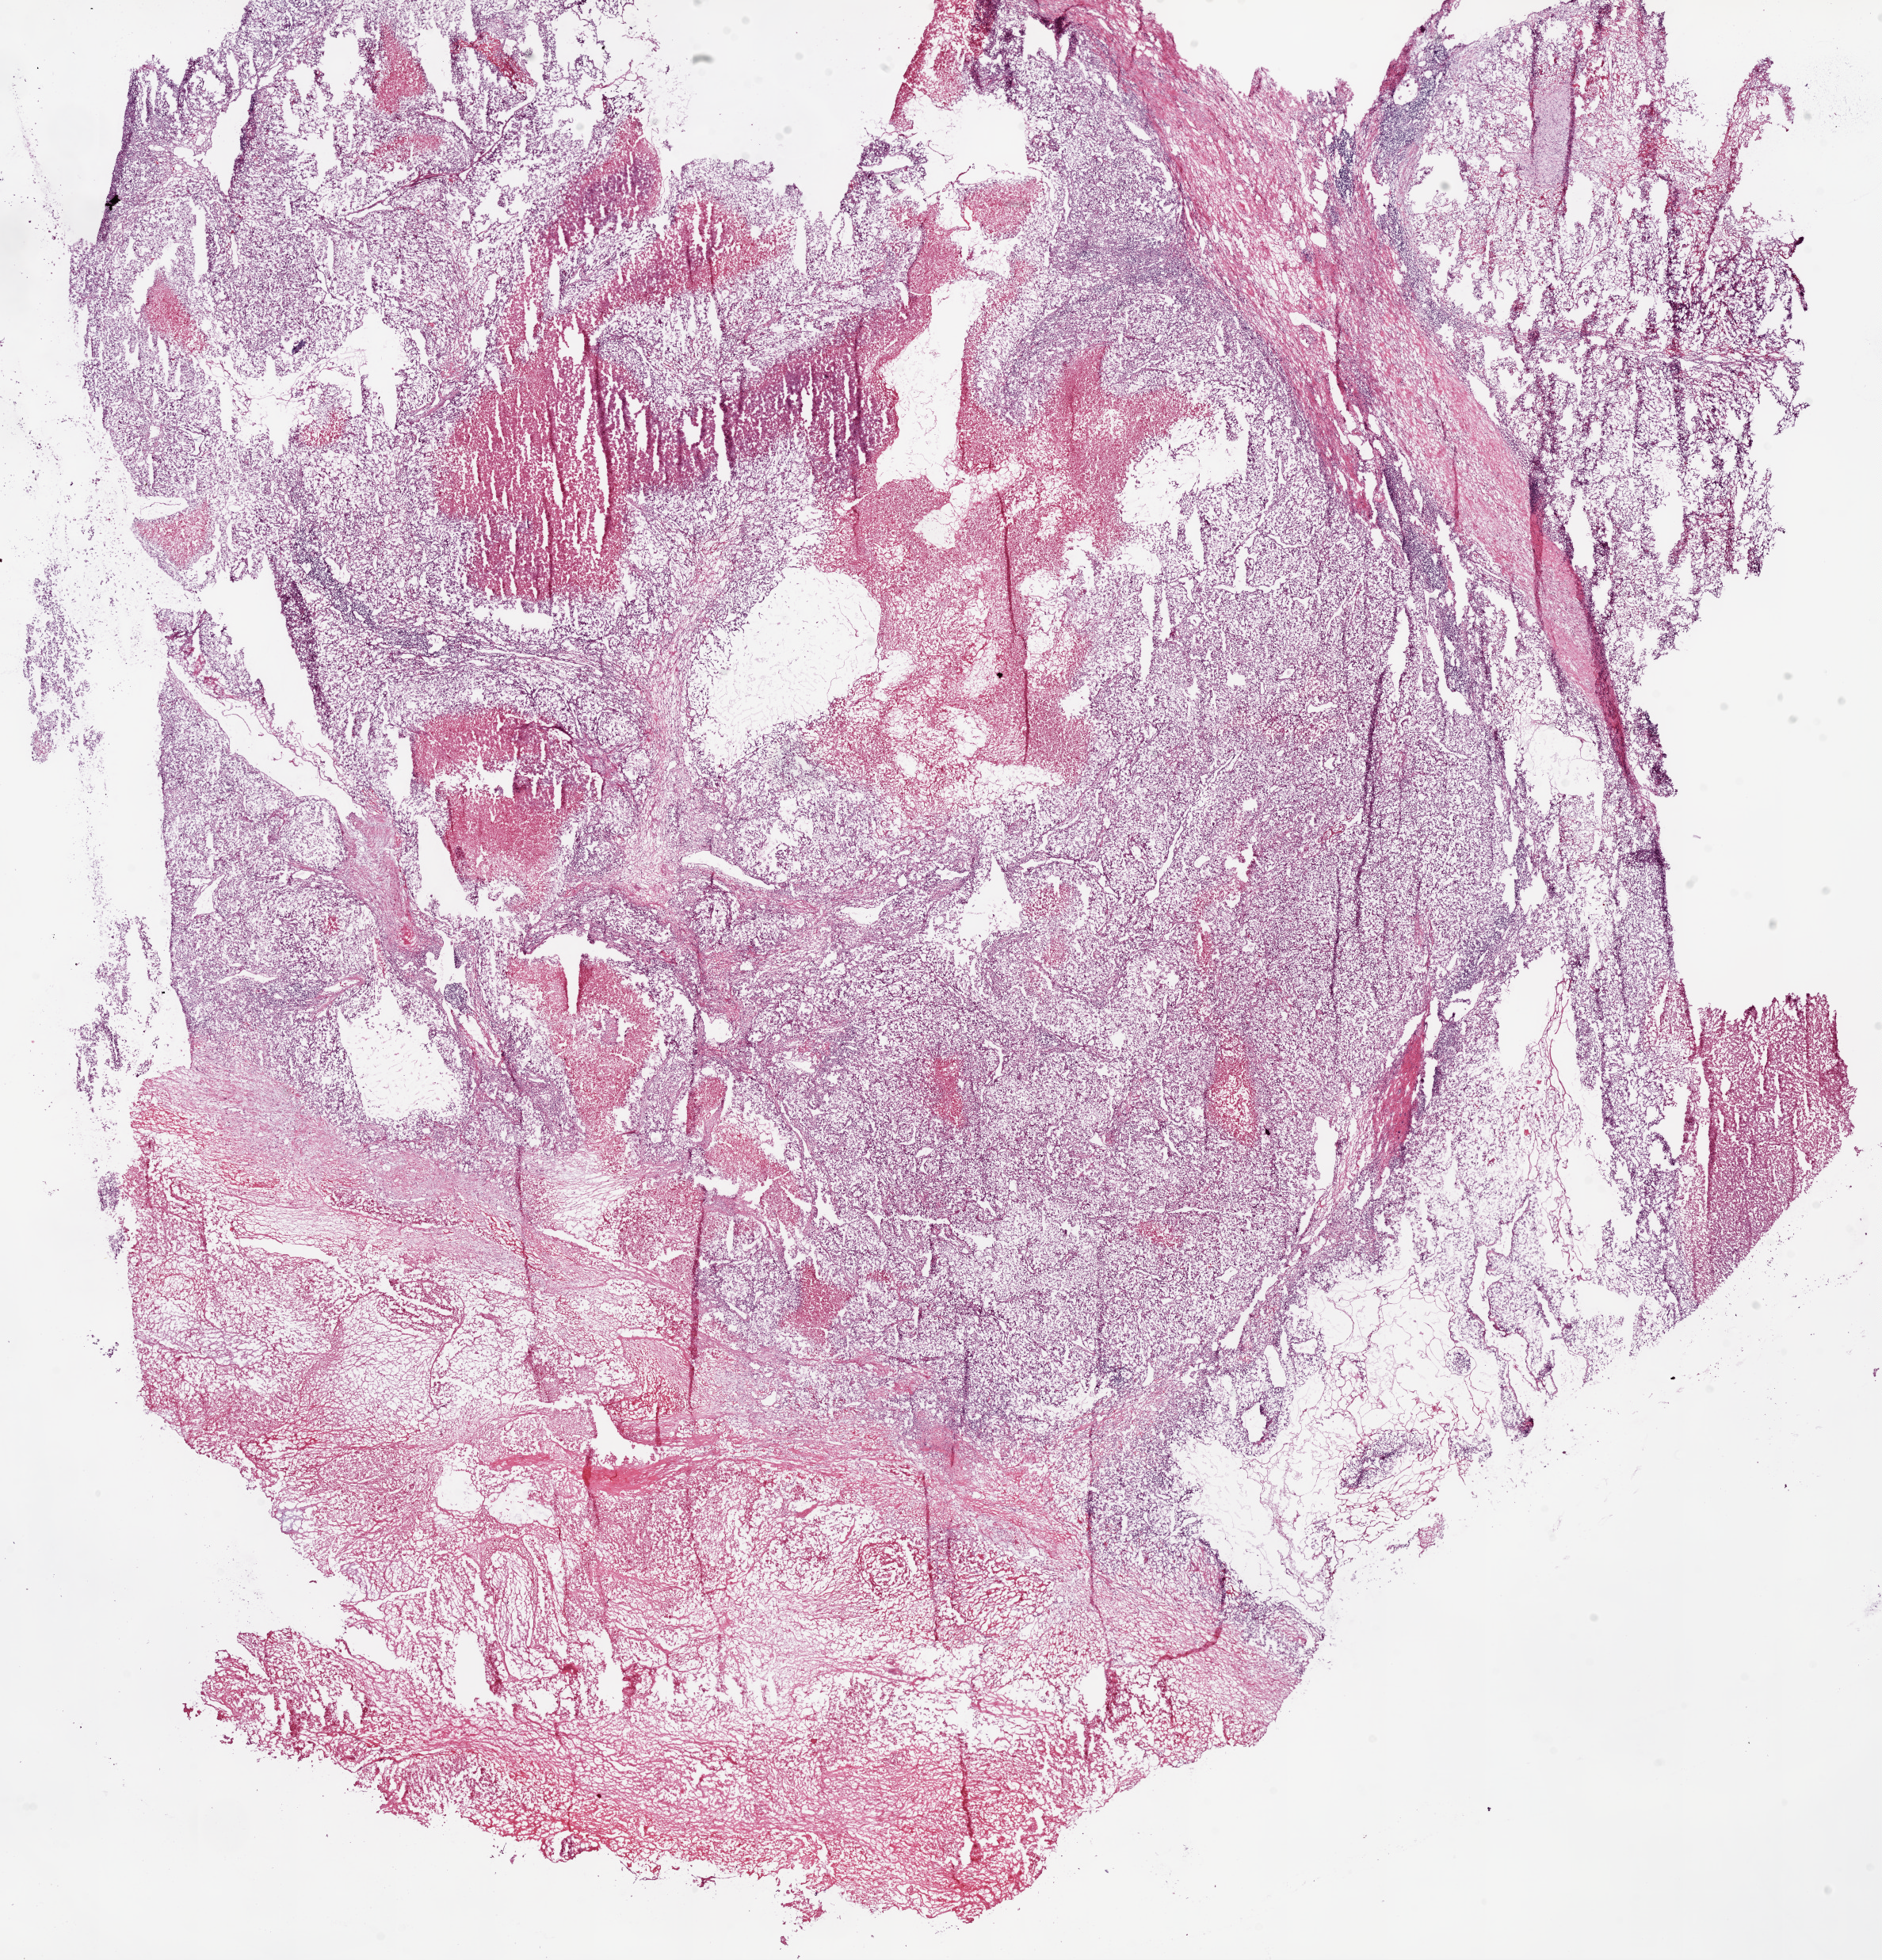
Digitized H&E-stained tissue section (whole slide) — whole scanned area (about 19.1 x 19.9 mm, from a 20x scan) shown as a low-resolution overview, frozen section from the bottom of the tissue portion, kidney, primary tumour sample. Male patient; age at initial diagnosis 60 years. Histologic grade: G4 (undifferentiated). Composition of this section per pathologist review: tumour cells 75%, tumour nuclei 65%, normal cells 0%, stromal cells 15%, necrosis 10%.
AJCC pathologic stage: IV. TNM: T4 NX M1. Pathologic diagnosis: Clear cell adenocarcinoma, NOS.